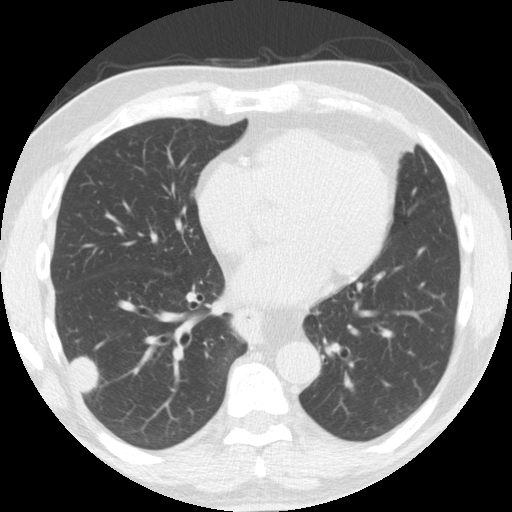
Low-dose screening chest CT, axial slice. Second annual screen. Lung window (W 1500 / L -600 HU). 2.5 mm slice thickness. Standard (soft-tissue) reconstruction kernel (STANDARD). Male participant, aged 61 years at enrolment.
- Lesion marked by an expert reader, bounding box [x1, y1, x2, y2] px = [45, 322, 113, 399].
- Reader record for this screening exam (exam-level; its link to the box is not recorded): non-calcified nodule or mass ≥4 mm, right lower lobe, 33 × 19 mm, smooth margins, soft tissue attenuation, pre-existing on the prior screen: yes; interval growth: yes.
- Participant outcome: lung cancer diagnosed 30 days after this screen — adenosquamous carcinoma, right lower lobe, poorly differentiated (G3), stage IV (AJCC 6th edition), 45 mm at pathology.